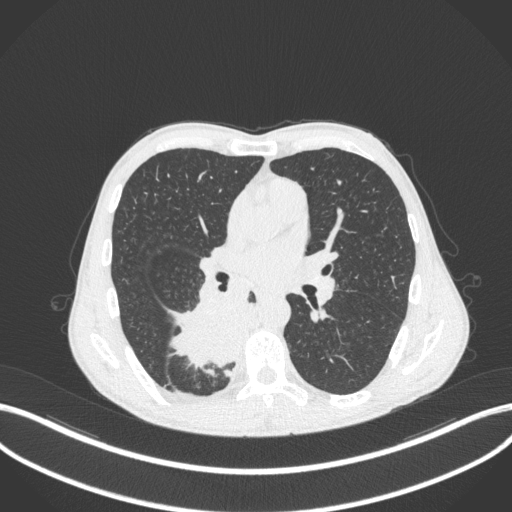
Chest CT, one axial slice; slice 200 of 371 in the series (ordered by position); lung window (W 1500 / L -600 HU); 1 mm slice thickness; 512 × 512 image matrix. Male patient, age 58 years. From the clinical record (not read from this slice): clinical TNM (as recorded): T3 N1 M1.
Annotated regions visible in this slice (bounding box drawn by a radiologist):
- lung tumour (recorded histology: squamous cell carcinoma): bounding box <163,286,253,378> (left, top, right, bottom; pixels)